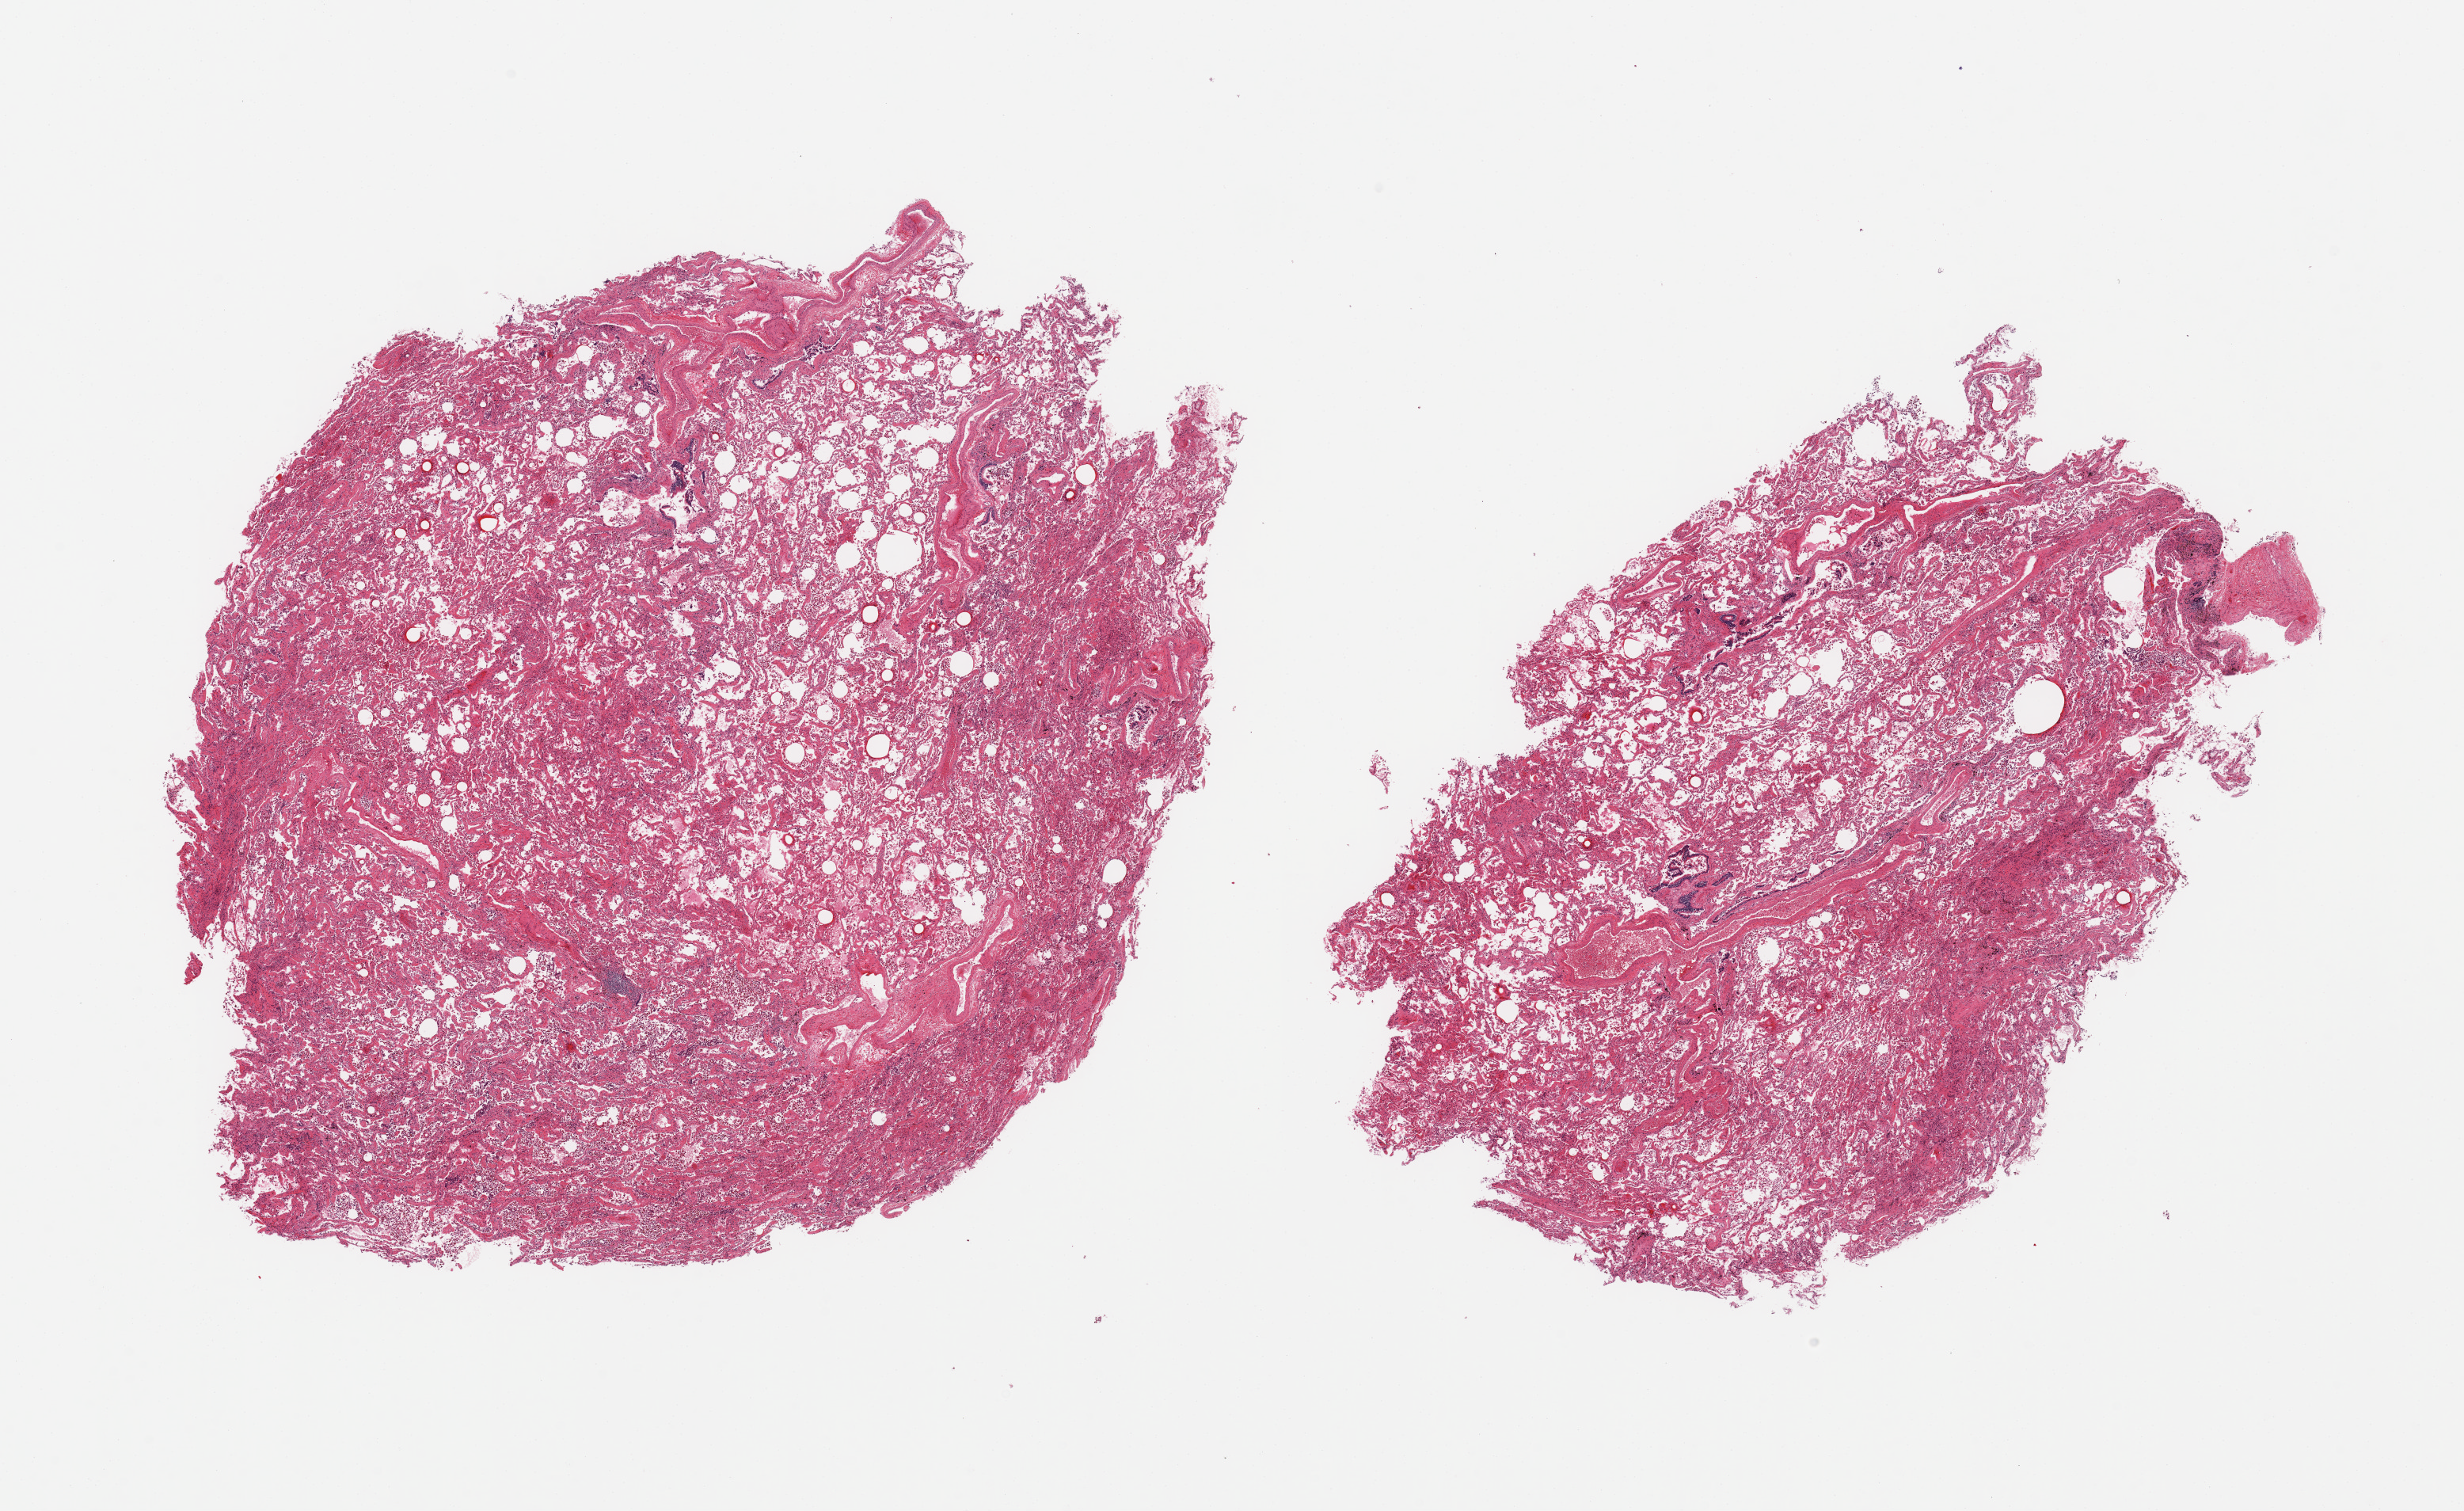
Whole-slide image, hematoxylin and eosin (H&E) stain, whole scanned area (about 24.6 x 15.1 mm) shown as a low-resolution overview; PAXgene-fixed, paraffin-embedded tissue; sampled site (target tissue): lung; donor tissue sample. Donor sex: male.
• review note (as recorded): 2 pieces; moderate interstitial fibrosis; numerous alveolar macrophages and desquamated alveolar lining cells